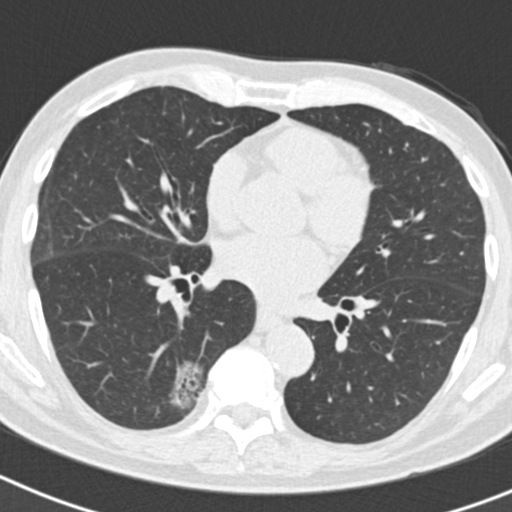
Low-dose screening chest CT, axial slice; second annual screen; lung window (W 1500 / L -600 HU); 2 mm slice thickness; 120 kVp; slice 92 of 186 in the series; 512 × 512 image matrix, field of view 300 × 300 mm. Male participant, aged 70 years at enrolment. Current smoker at enrolment.
Expert reader's lesion annotation, bounding box (x1, y1, x2, y2) in pixels: (126, 362, 206, 431). The screening reader recorded 5 non-calcified nodules or masses ≥4 mm on this exam; which of them this box marks is not recorded. Official screen result: positive, other. Later outcome: lung cancer diagnosed 622 days after this screen (after the third annual screen) — bronchiolo-alveolar adenocarcinoma, NOS, right lower lobe, poorly differentiated (G3), stage IB (AJCC 6th edition), 30 mm at pathology.